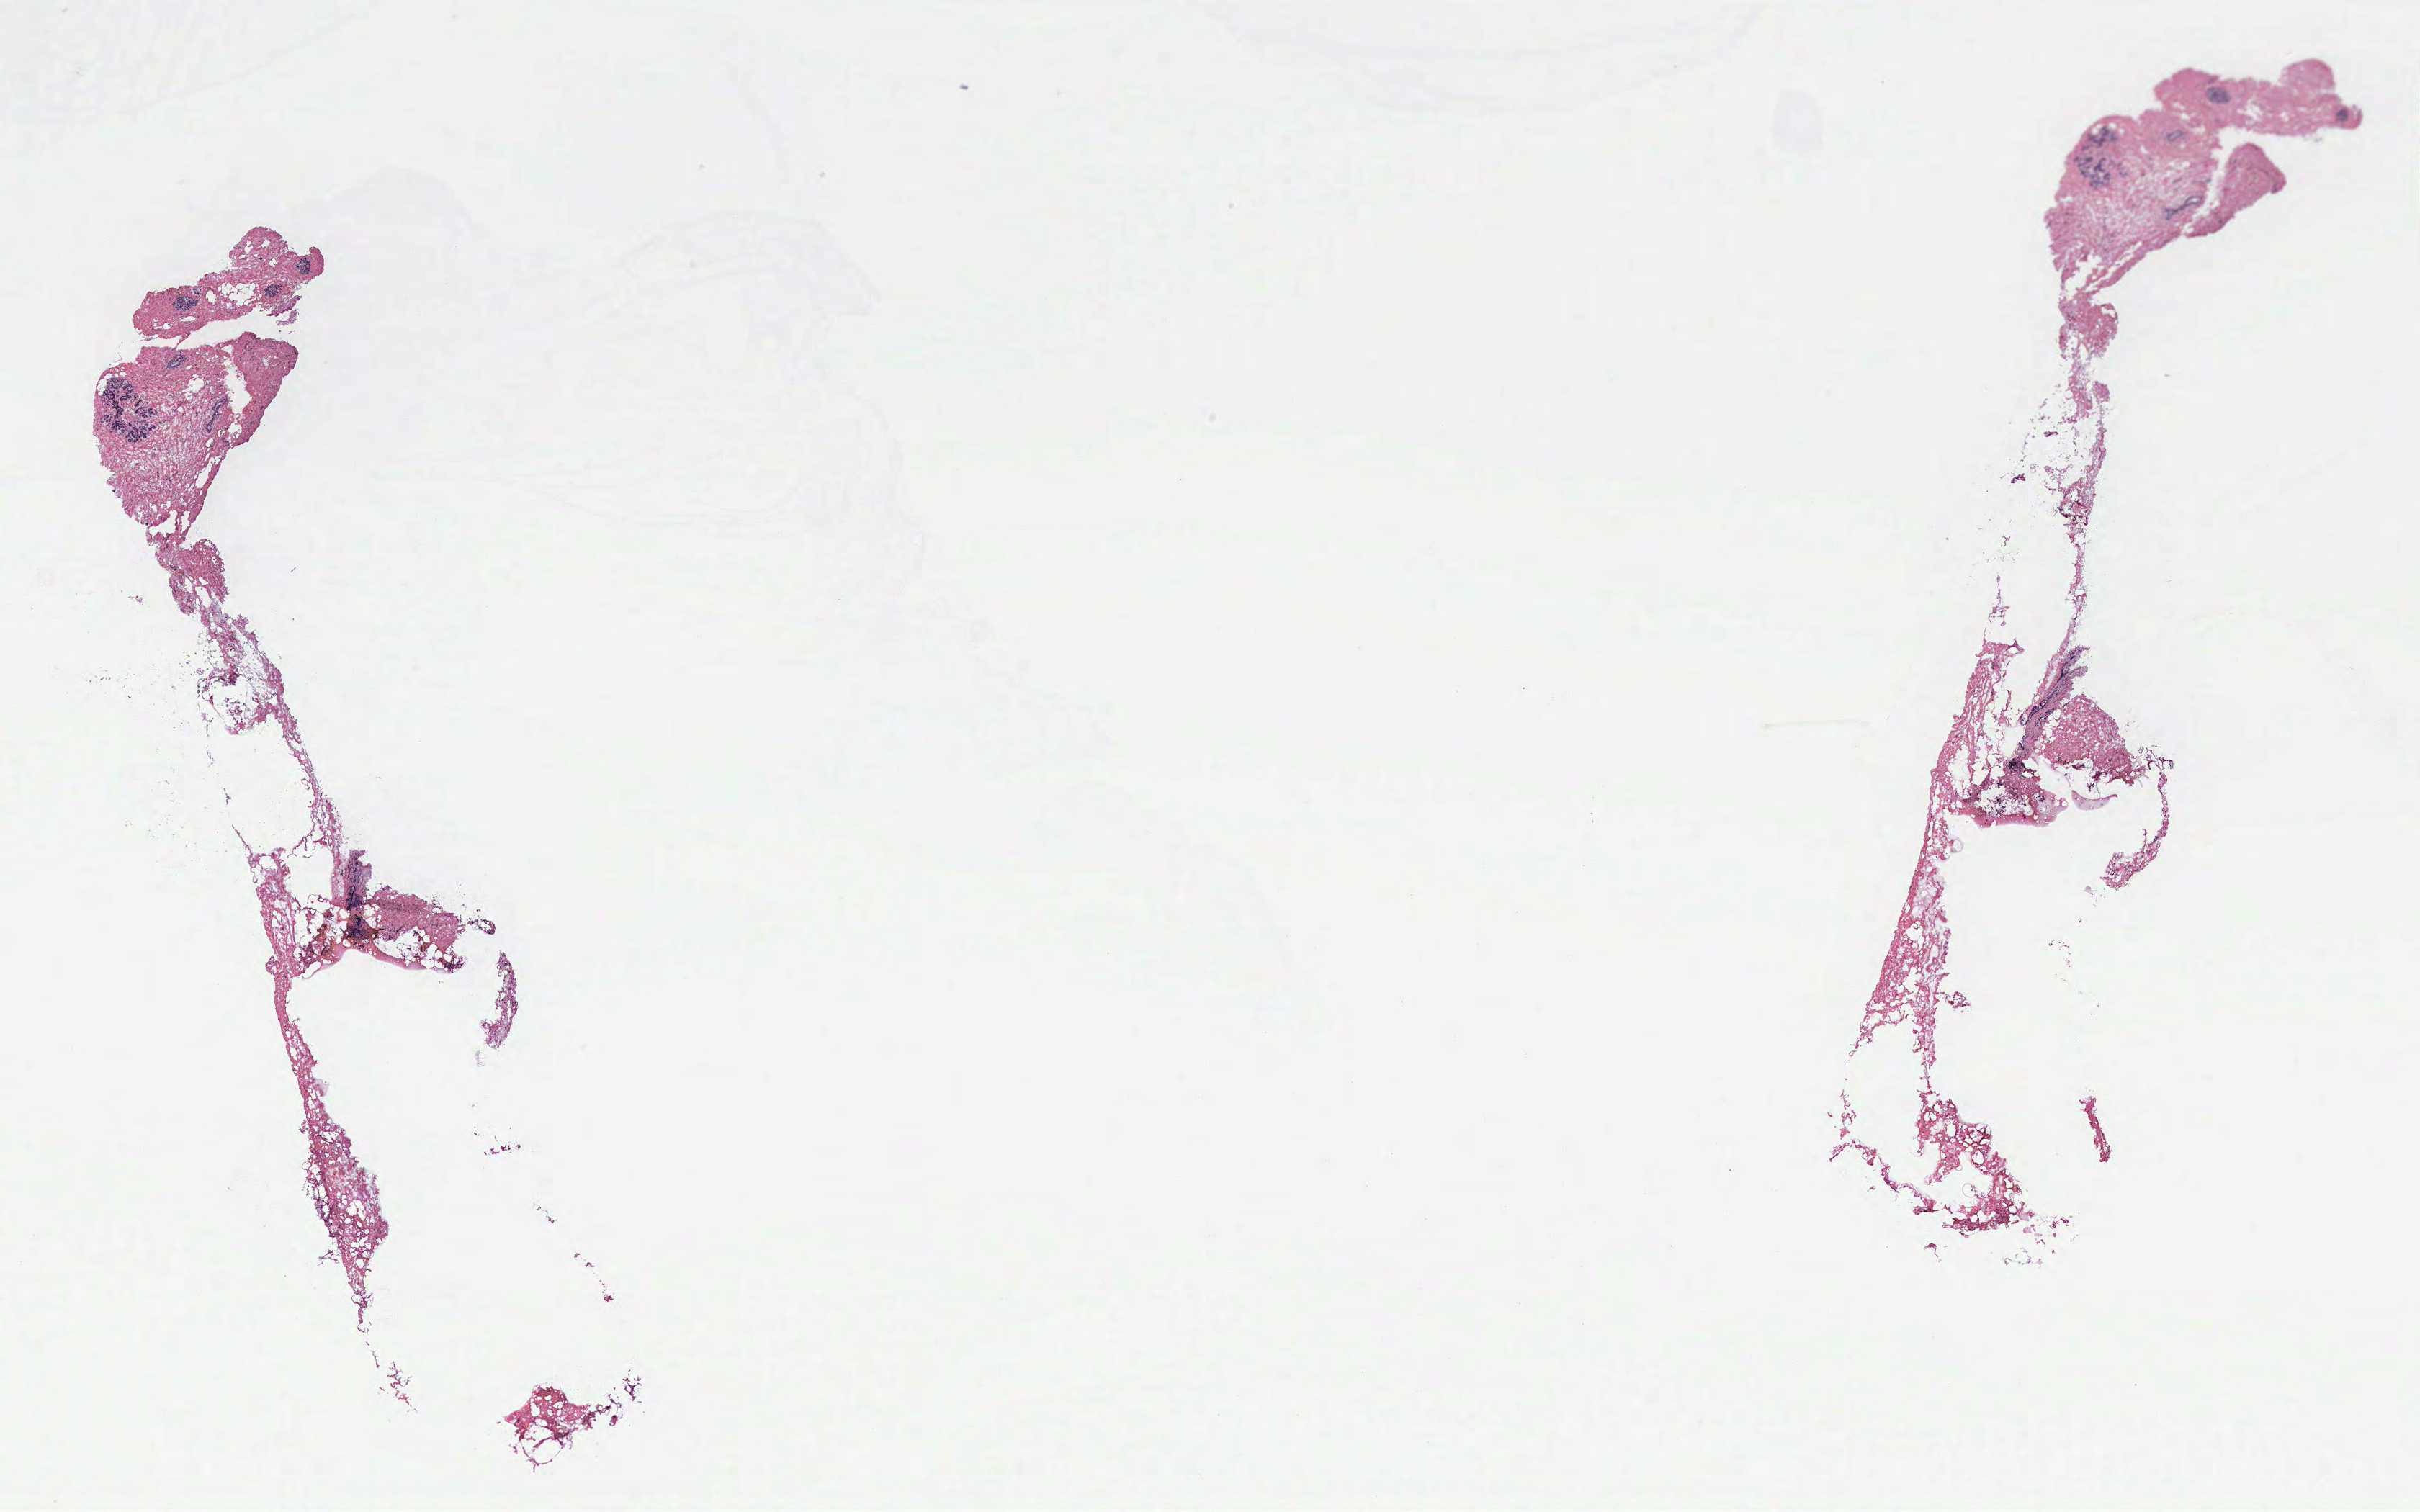
H&E whole-slide image — a low-resolution overview of the entire scanned area, about 26.9 x 16.8 mm (acquisition: 40x scan), breast, tissue type not recorded.
Patient diagnosis (cohort enrolment): breast cancer (breast).